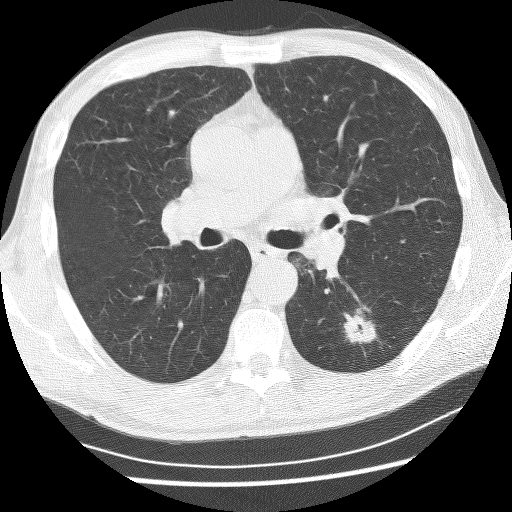
Axial slice from a low-dose chest CT screening exam. Baseline annual screen. Lung window (W 1500 / L -600 HU). 2.5 mm slice thickness. Lung (sharp) reconstruction kernel (BONE). 120 kVp. Slice 107 of 253 in the series. 512 × 512 image matrix, field of view 340 × 340 mm. Male, age 62 years at enrolment. Current smoker at enrolment.
Lesion marked by an expert reader, bounding box <330,307,382,352> (left, top, right, bottom; pixels). Screening reader's record for this exam (one nodule recorded; not confirmed to be the boxed lesion): non-calcified nodule or mass ≥4 mm, left lower lobe, 21 × 17 mm, spiculated (stellate) margins, soft tissue attenuation. Official screen result: positive, change unspecified: nodule(s) >= 4 mm or enlarging nodule(s), mass(es), or other non-specific abnormalities suspicious for lung cancer. Later outcome: lung cancer diagnosed 58 days after this screen — non-small cell carcinoma, left lower lobe, poorly differentiated (G3), stage IA (AJCC 6th edition), 11 mm at pathology.